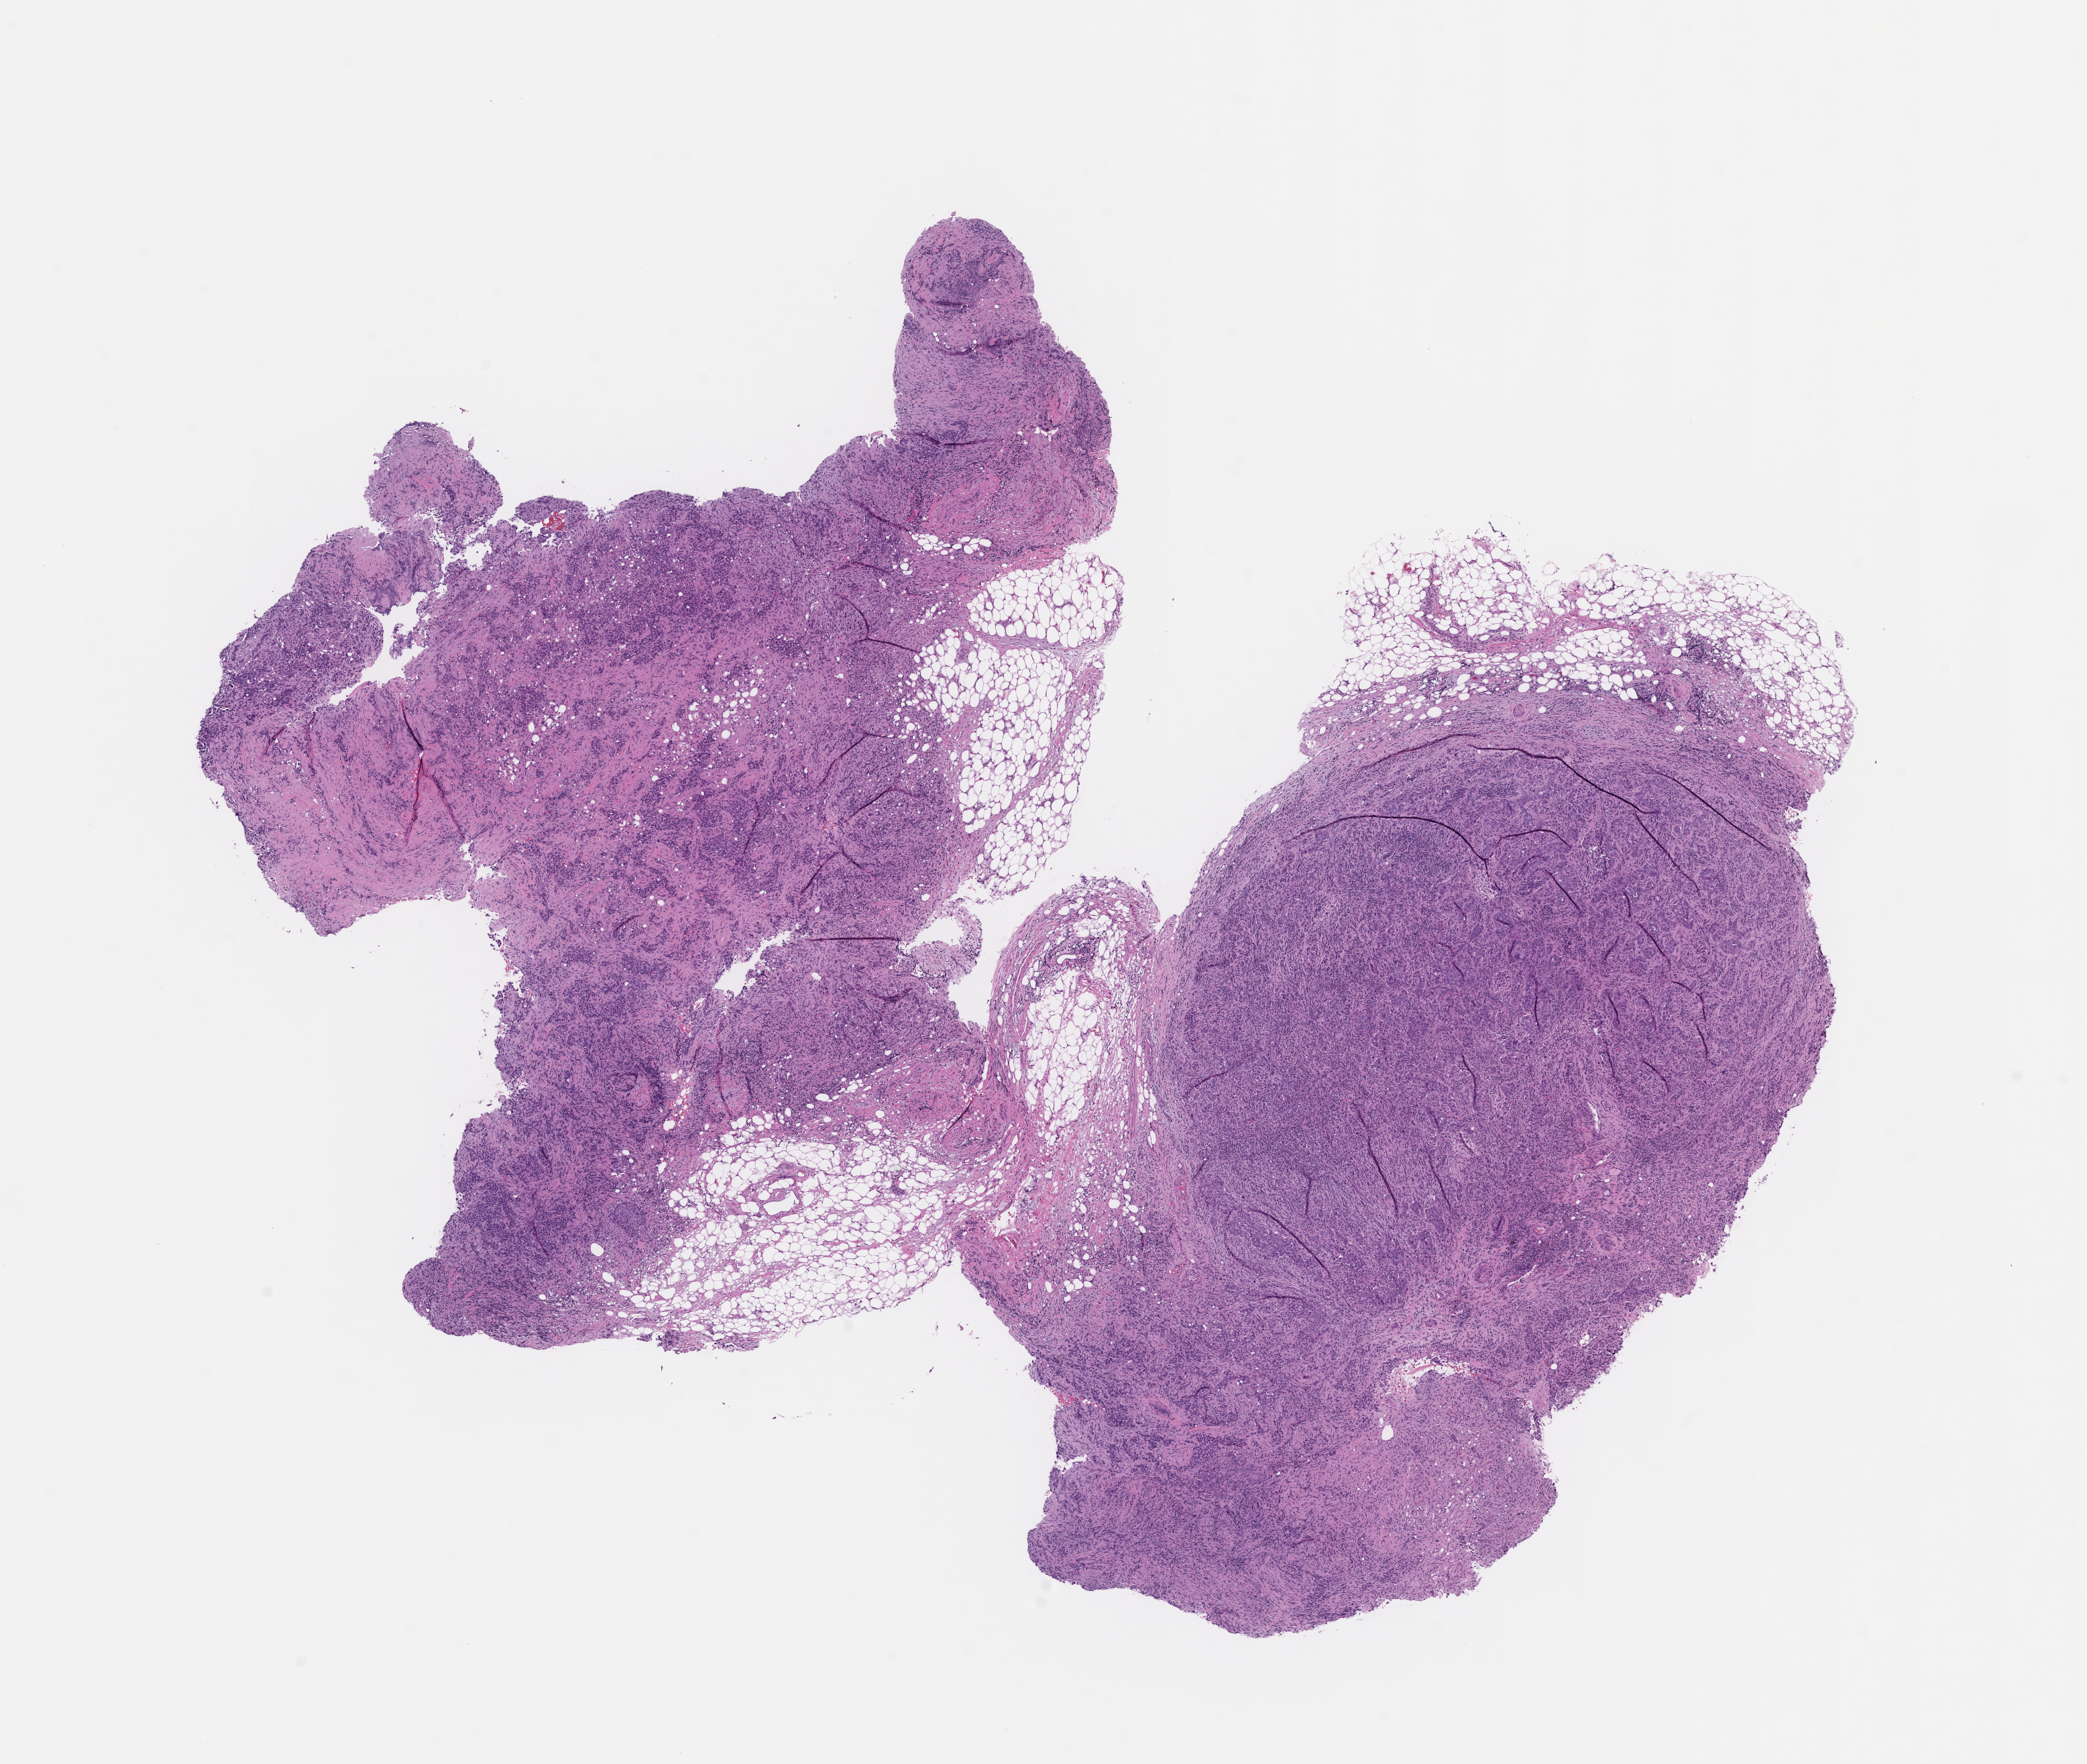
Haematoxylin and eosin whole-slide image — whole scanned area (about 12.6 x 10.6 mm) shown as a low-resolution overview. Formalin-fixed, paraffin-embedded (FFPE) tissue. Specimen time point: collected at baseline (before treatment). Patient: female.
This section: metastasis (sampled organ not recorded). Primary diagnosis of the patient: Non-Small Cell Lung Carcinoma.